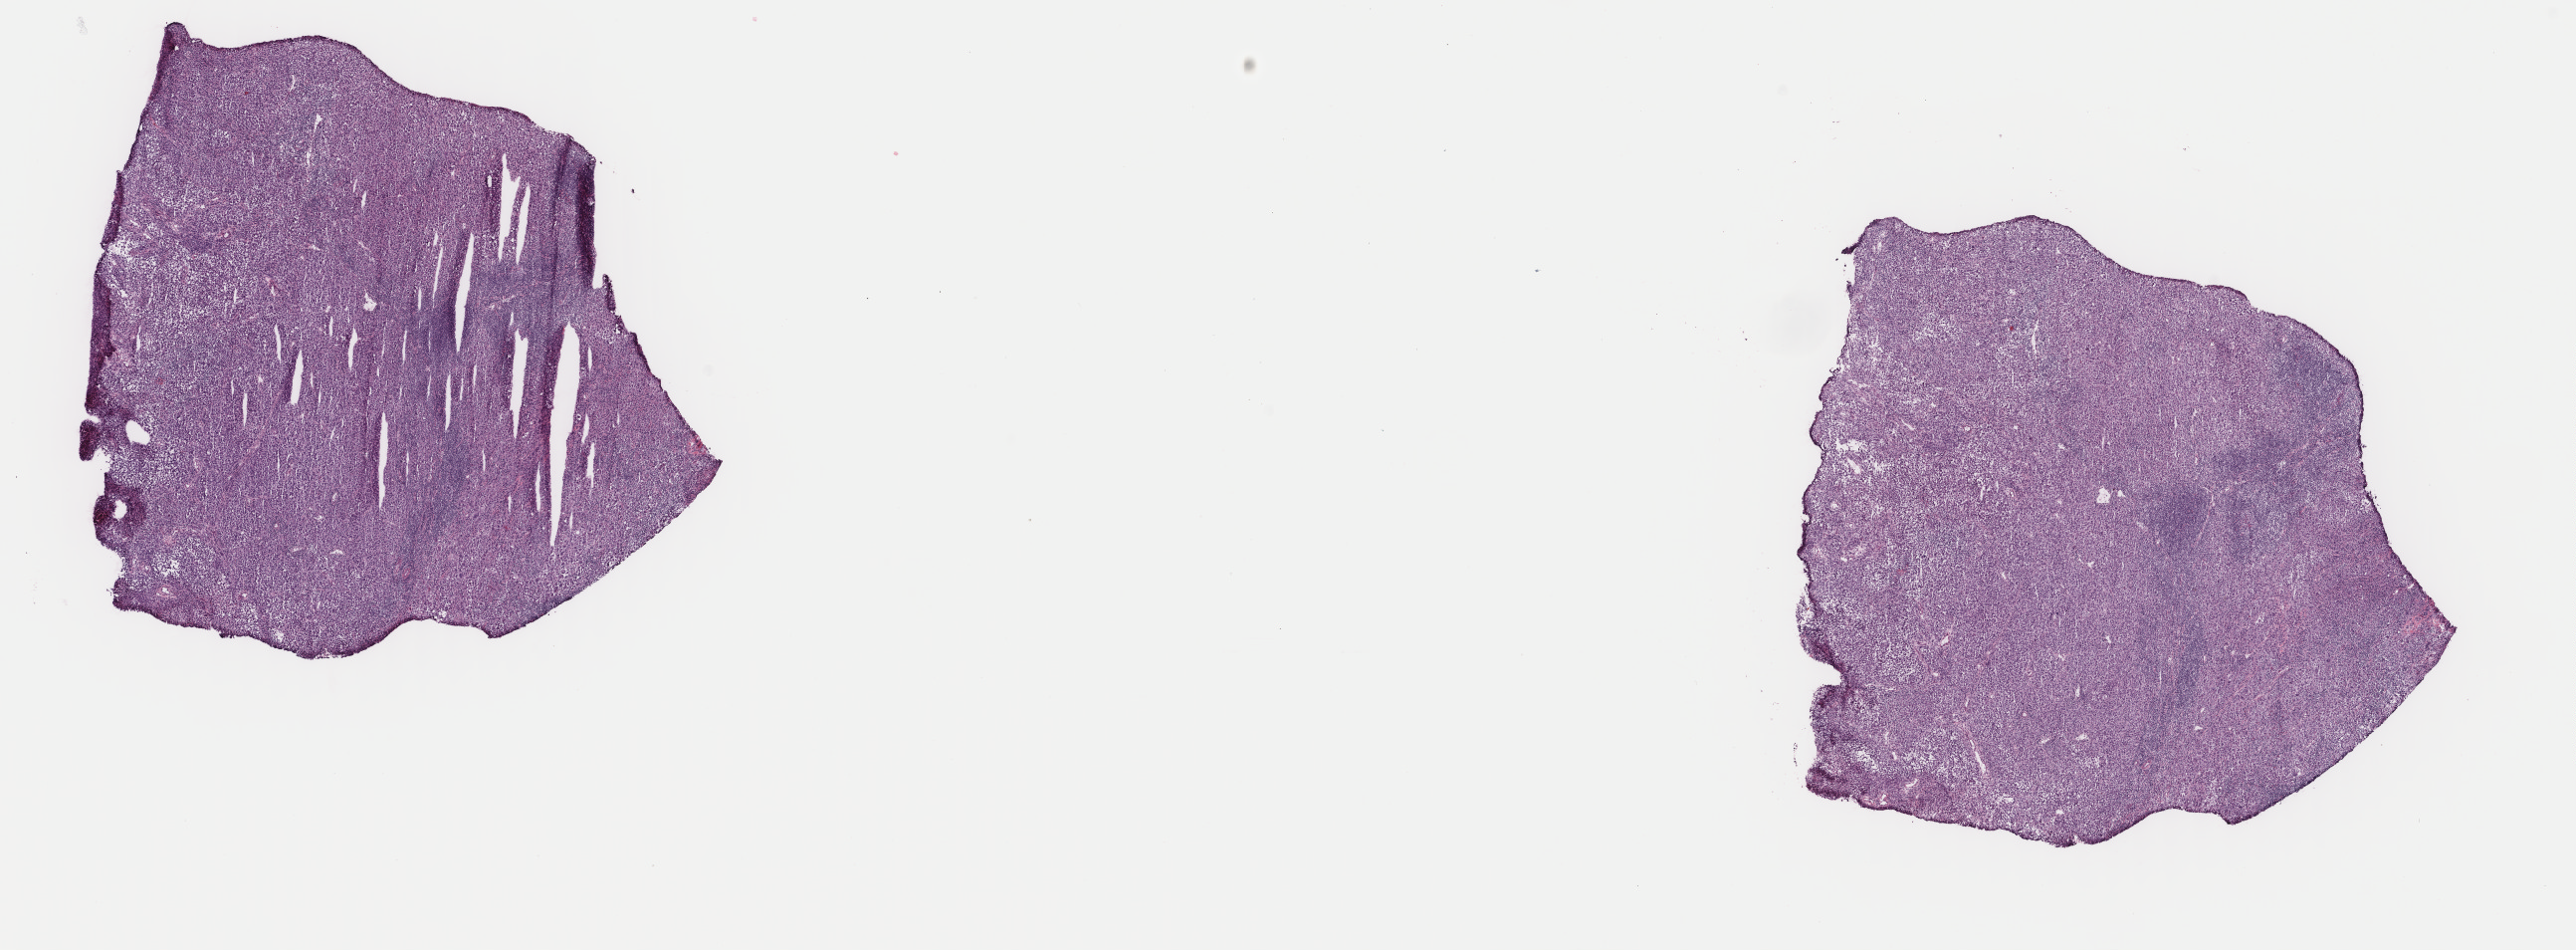
Digitized Hematoxylin and eosin (H&E) stained tissue section (whole slide) — whole scanned area (about 20.5 x 7.6 mm) shown as a low-resolution overview, frozen section from the top of the tissue portion, metastatic tumour sample, sampled site not recorded. Patient: female, age at initial diagnosis 38 years. Composition of this section per pathologist review: tumour cells 100%, tumour nuclei 80%, normal cells 0%, stromal cells 0%, necrosis 0%. Infiltration values recorded for this section: lymphocyte infiltration 1%, monocyte infiltration 0%, neutrophil infiltration 0%.
This section: metastatic tumour tissue. Patient diagnosis: Malignant melanoma, NOS.